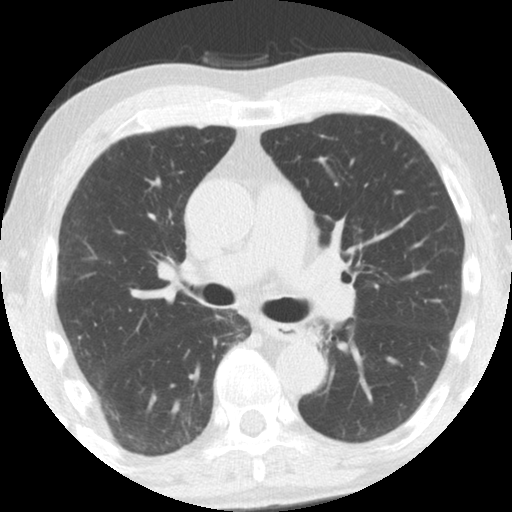
Axial slice from a low-dose chest CT screening exam; third screening round (two years after baseline); lung window (W 1500 / L -600 HU); 2.5 mm slice thickness; slice 52 of 108 in the series. Male, age 61 years at enrolment. Former smoker at enrolment.
Expert reader's lesion annotation, box from (x=293, y=316) to (x=345, y=362) px. Screening reader's record for this exam: no non-calcified nodule ≥4 mm recorded. Lung cancer was diagnosed 363 days after this screen: squamous cell carcinoma, NOS, left upper lobe, left lower lobe, well differentiated (G1), stage IIB (AJCC 6th edition), 100 mm at pathology.